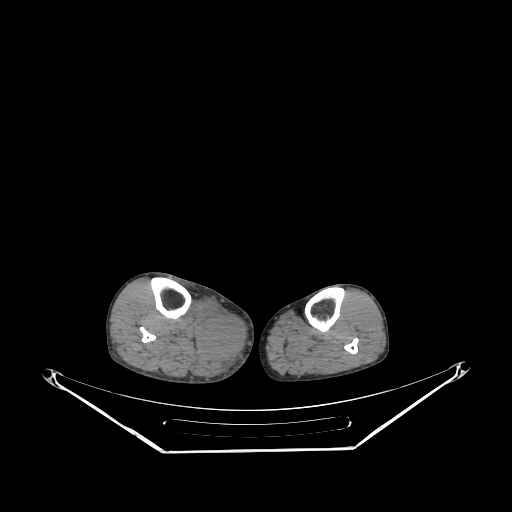
CT of an extremity soft-tissue mass (from a PET/CT study), one axial slice. Reconstruction kernel SOFT. 140 kVp. Soft-tissue window (W 400 / L 40 HU). 3.75 mm slice thickness. 512 × 512 image matrix. Male patient. From the clinical record (not read from this slice): histological type: pleiomorphic liposarcoma; grade: high; site of the primary tumour: right calf.
Annotated regions visible in this slice (expert contour drawn on MRI and transferred to this co-registered scan by the dataset authors):
- gross tumour volume including surrounding oedema: bounding box [x1, y1, x2, y2] px = [199, 308, 245, 362]
- gross tumour volume (mass): [203, 317, 245, 357]